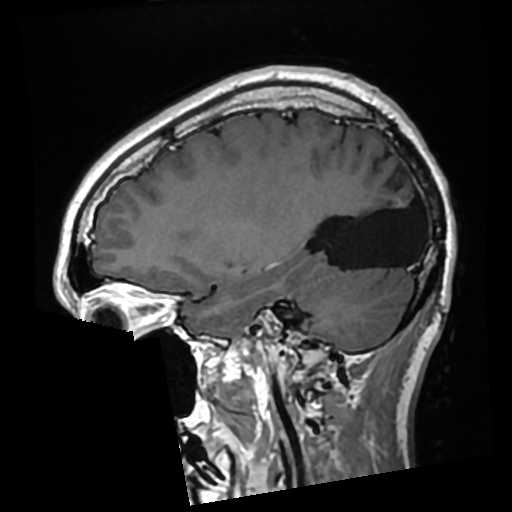
Brain MRI from a brain-tumour surgery series, one sagittal slice; slice 100 of 276 in the series (ordered by position); T1-weighted post-contrast; 0.7 mm slice thickness; 512 × 512 image matrix, field of view 250 × 250 mm. From the clinical record (not read from this slice): histopathology: Glioma with ependymal features; WHO grade: 2.
Structures marked on this image (manually delineated by an expert):
- previous resection cavity: bounding box [x1, y1, x2, y2] px = [325, 182, 419, 268]
- tumour: [397, 199, 403, 207]